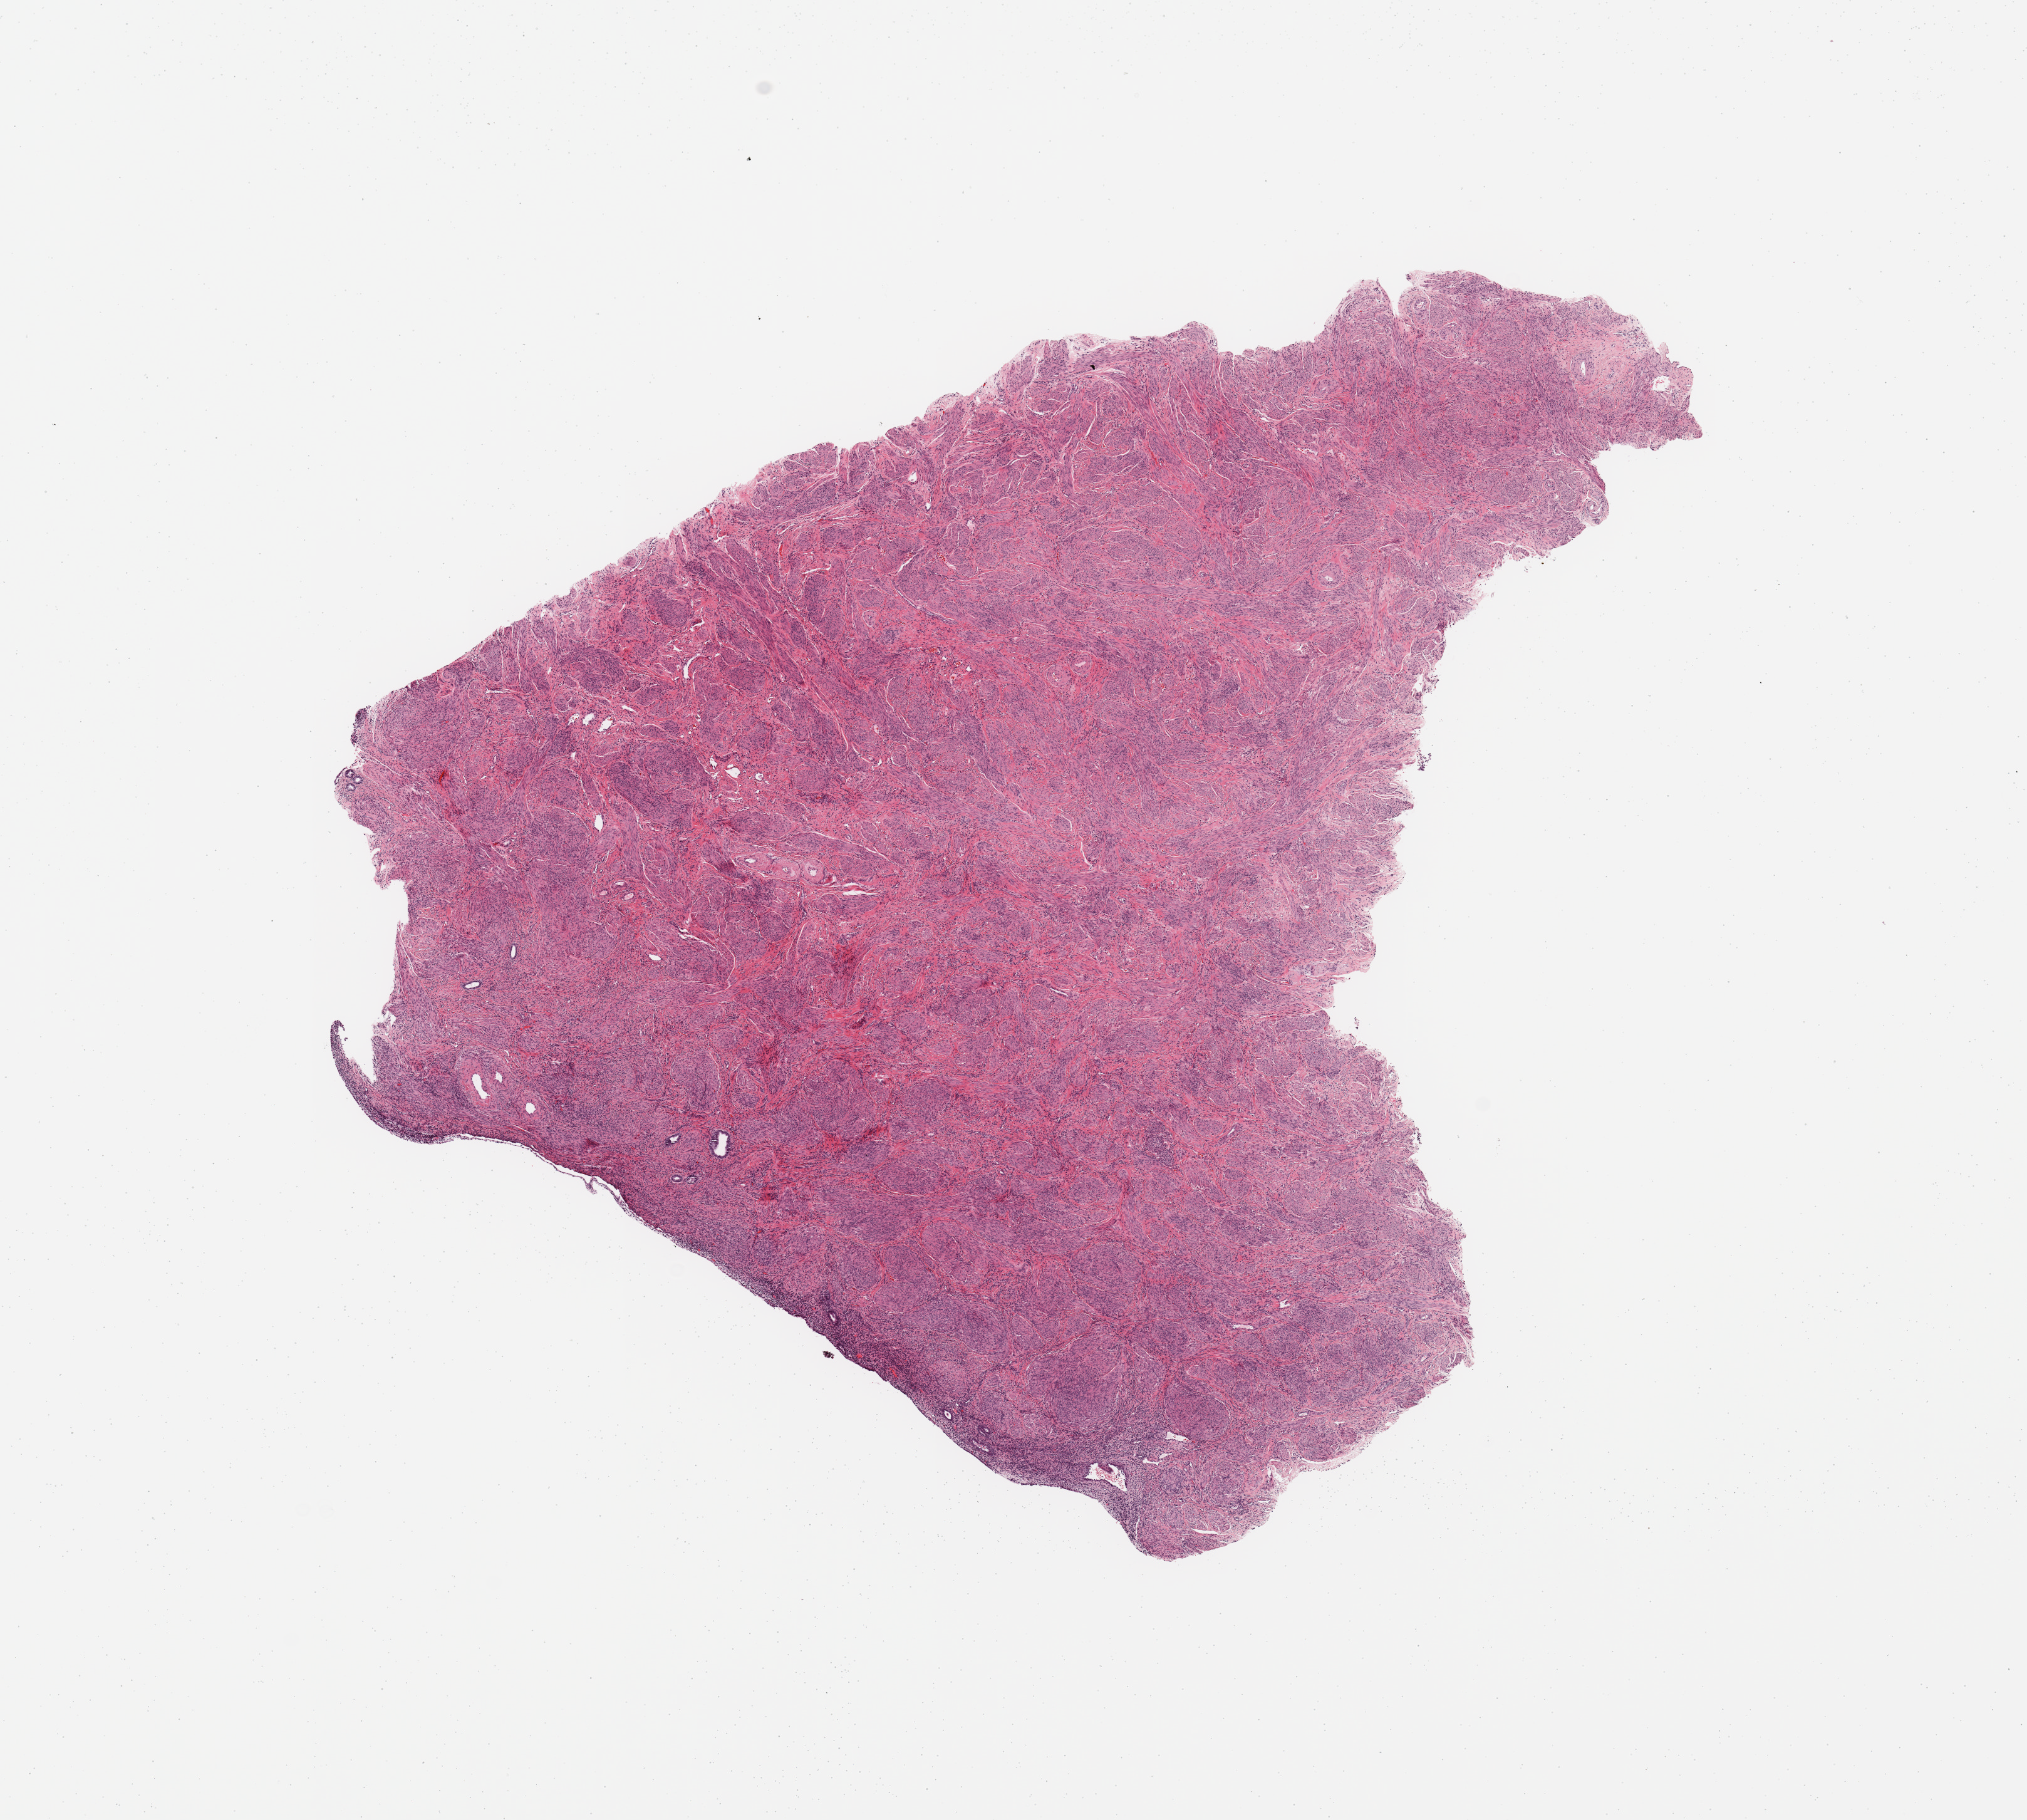
Whole-slide histology image, Hematoxylin and eosin (H&E) stained — shown as a low-resolution overview of the whole scanned area (about 12.8 x 11.5 mm). Normal (non-tumour) tissue sample, sampled site: uterus. Patient: female, age 75 years.
This section: normal (non-tumour) tissue from the same patient. Patient diagnosis: Endometrioid adenocarcinoma, NOS.